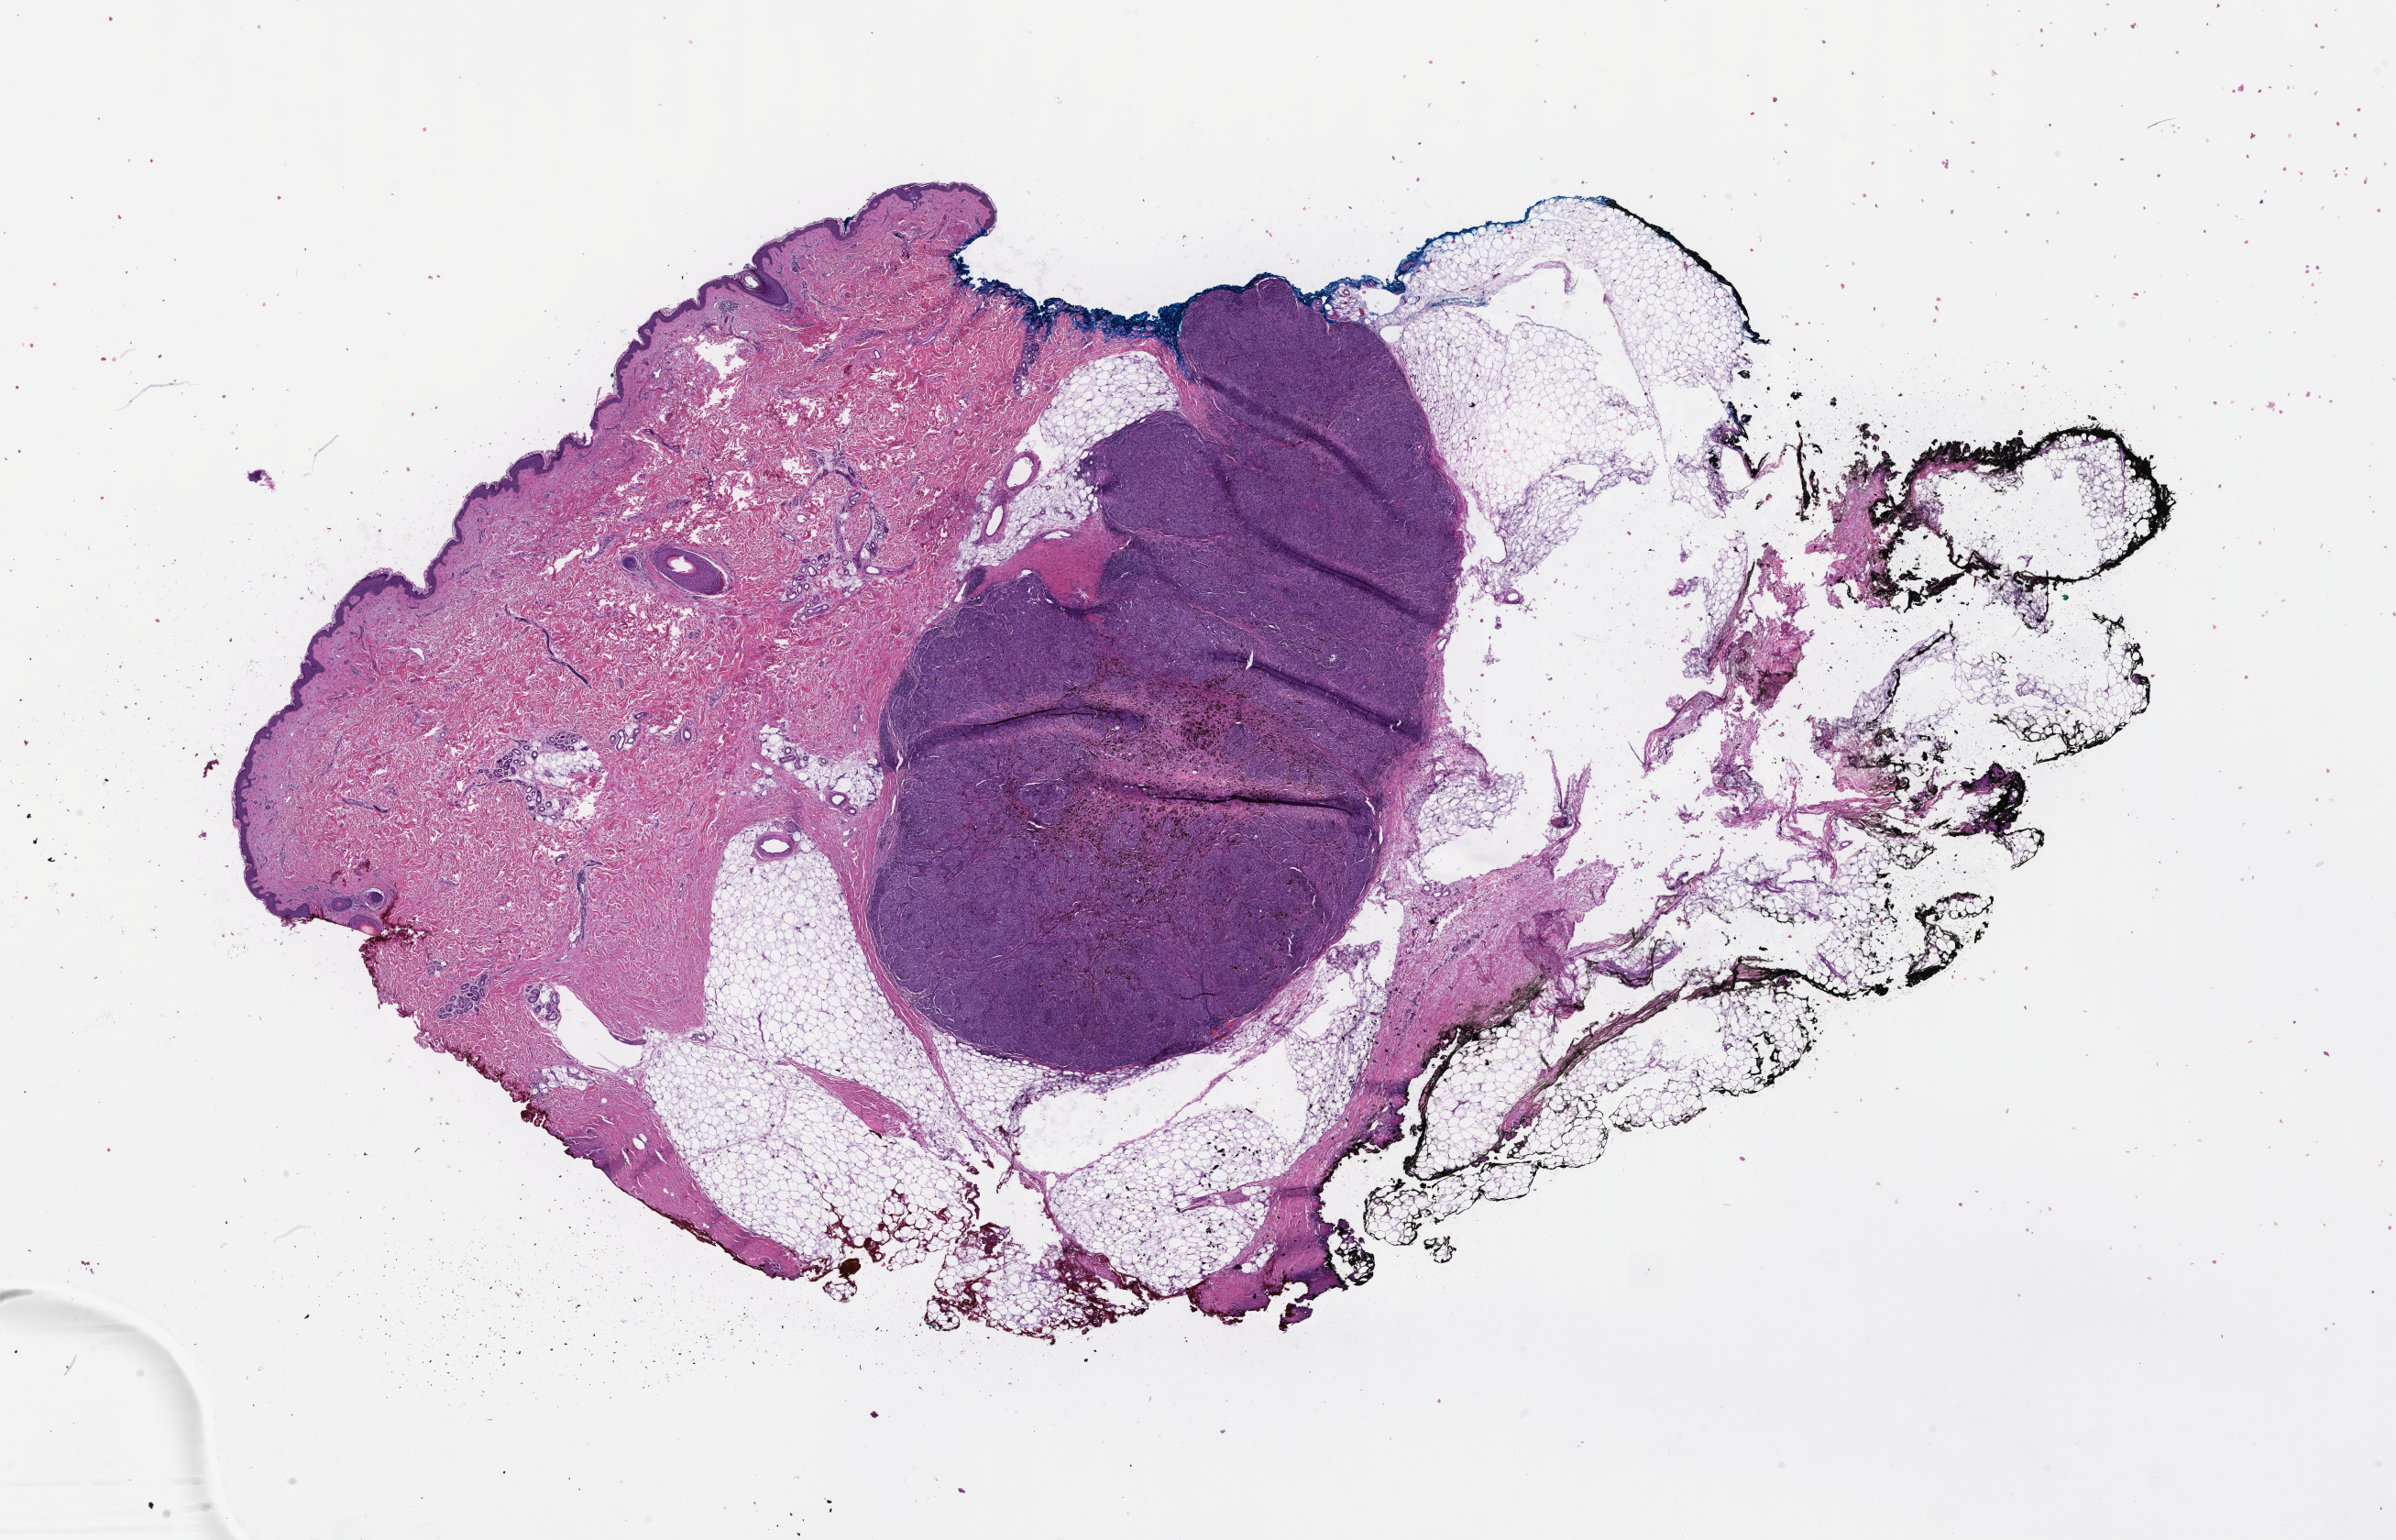
Haematoxylin and eosin whole-slide image, low-resolution overview of the scanned area, about 21.1 x 13.6 mm; formalin-fixed, paraffin-embedded (FFPE) tissue; tissue site: skin; archival tissue. Patient sex: male.
This section: primary tumour tissue. Diagnosis: Melanoma.